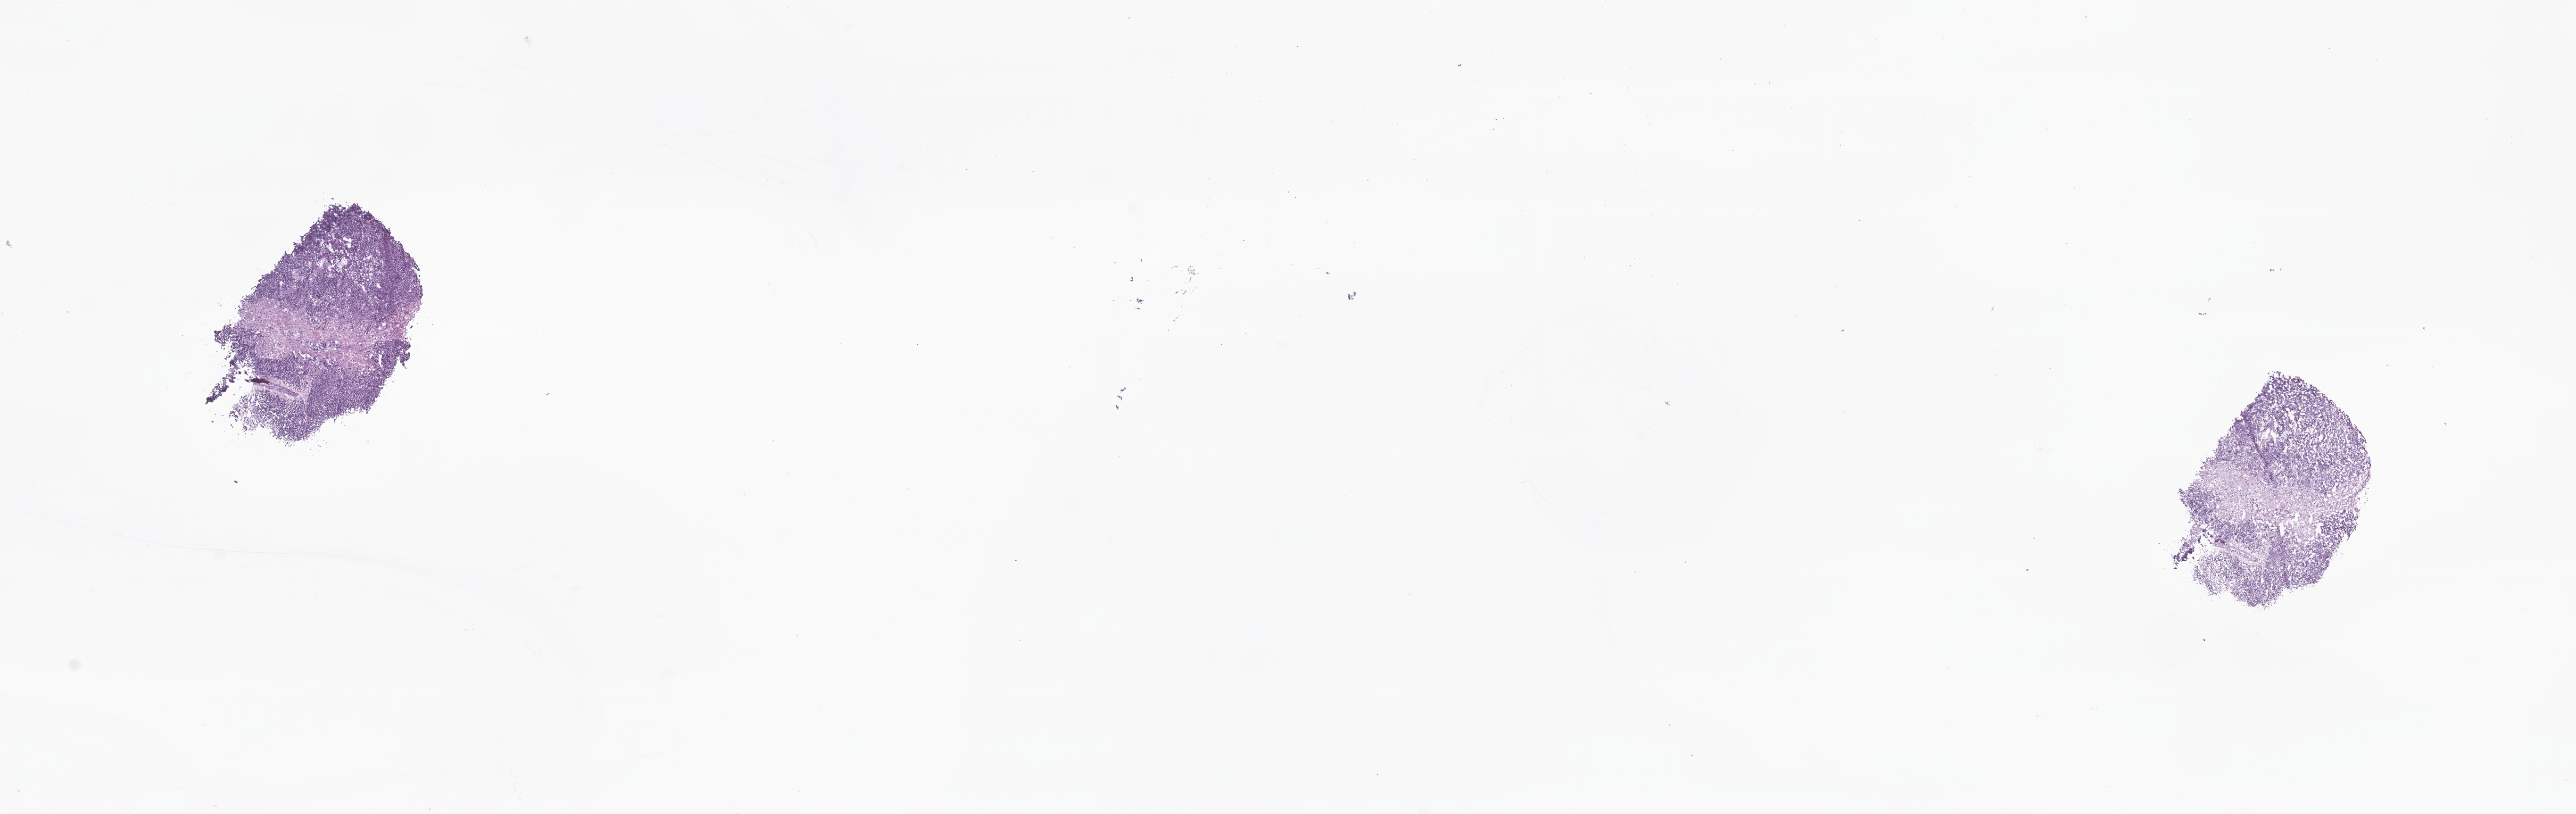
Digitized haematoxylin and eosin-stained section of tumor tissue from the soft tissues of head and neck — a low-resolution overview of the entire scanned area, about 23.0 x 7.3 mm. Frozen section. Patient female; age 63 months (5 years 3 months).
- diagnosis (ICD-O-3 morphology term): Rhabdomyosarcoma, NOS